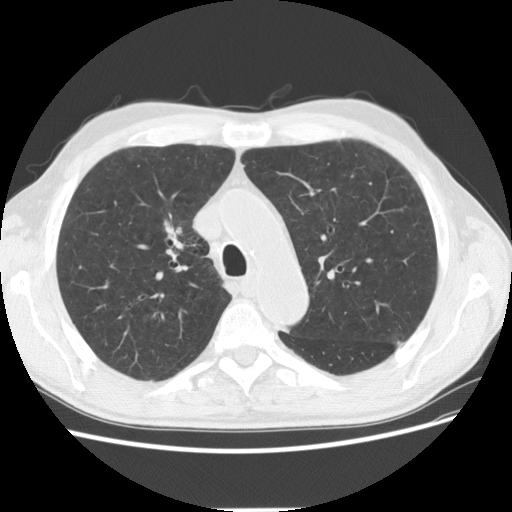
Axial slice from a low-dose chest CT screening exam, first (baseline) screen, lung window (W 1500 / L -600 HU), standard (soft-tissue) reconstruction kernel (STANDARD), slice 41 of 135 in the series. Male, age 73 years at enrolment. Current smoker at enrolment.
Expert-annotated lung lesion, box from (x=142, y=204) to (x=204, y=261) px. The exam's reader record, not a measurement of the box and not confirmed to be the same lesion: non-calcified nodule or mass ≥4 mm, right upper lobe, 16 × 9 mm, spiculated (stellate) margins, soft tissue attenuation. Later outcome: lung cancer diagnosed 734 days after this screen (after the third annual screen) — squamous cell carcinoma, NOS, right upper lobe, poorly differentiated (G3), stage IIIB (AJCC 6th edition), 56 mm at pathology.